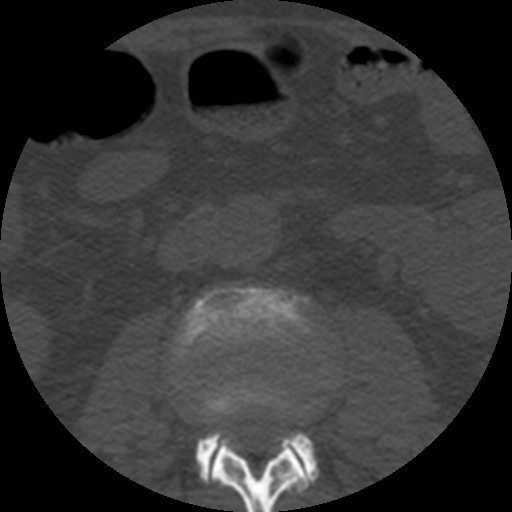
CT including the spine, one axial slice. Slice 137 of 508 in the series (ordered by position). 120 kVp. Bone window (W 1800 / L 400 HU). 1.25 mm slice thickness. 512 × 512 image matrix, field of view 160 × 160 mm. Patient age 57 years. Case-level facts recorded for this patient, not image findings: primary cancer: prostate.
Structures marked on this image (semi-automatic segmentation, software-assisted and operator-edited):
- L2 vertebra: bounding box <202,432,311,512> (left, top, right, bottom; pixels)
- L3 vertebra: <173,287,318,480>